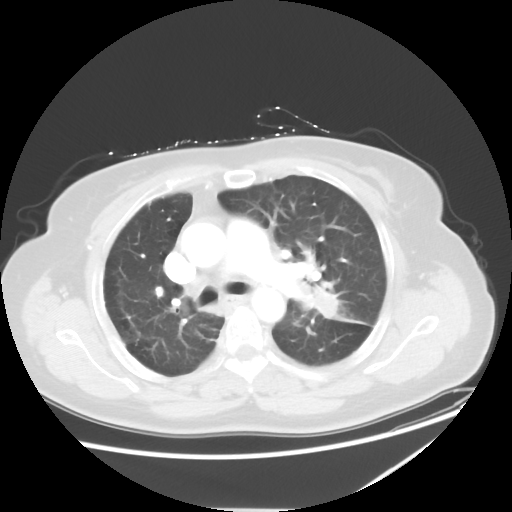
Chest CT, one axial slice; slice 36 of 54 in the series (ordered by position); reconstruction kernel STANDARD; 120 kVp; lung window (W 1500 / L -600 HU); 512 × 512 image matrix. Female patient, age 61 years. From the clinical record (not read from this slice): clinical TNM (as recorded): T1c N3 M1.
Annotated regions visible in this slice (bounding box drawn by a radiologist):
- lung tumour (recorded histology: adenocarcinoma): bounding box [x1, y1, x2, y2] px = [308, 282, 372, 331]